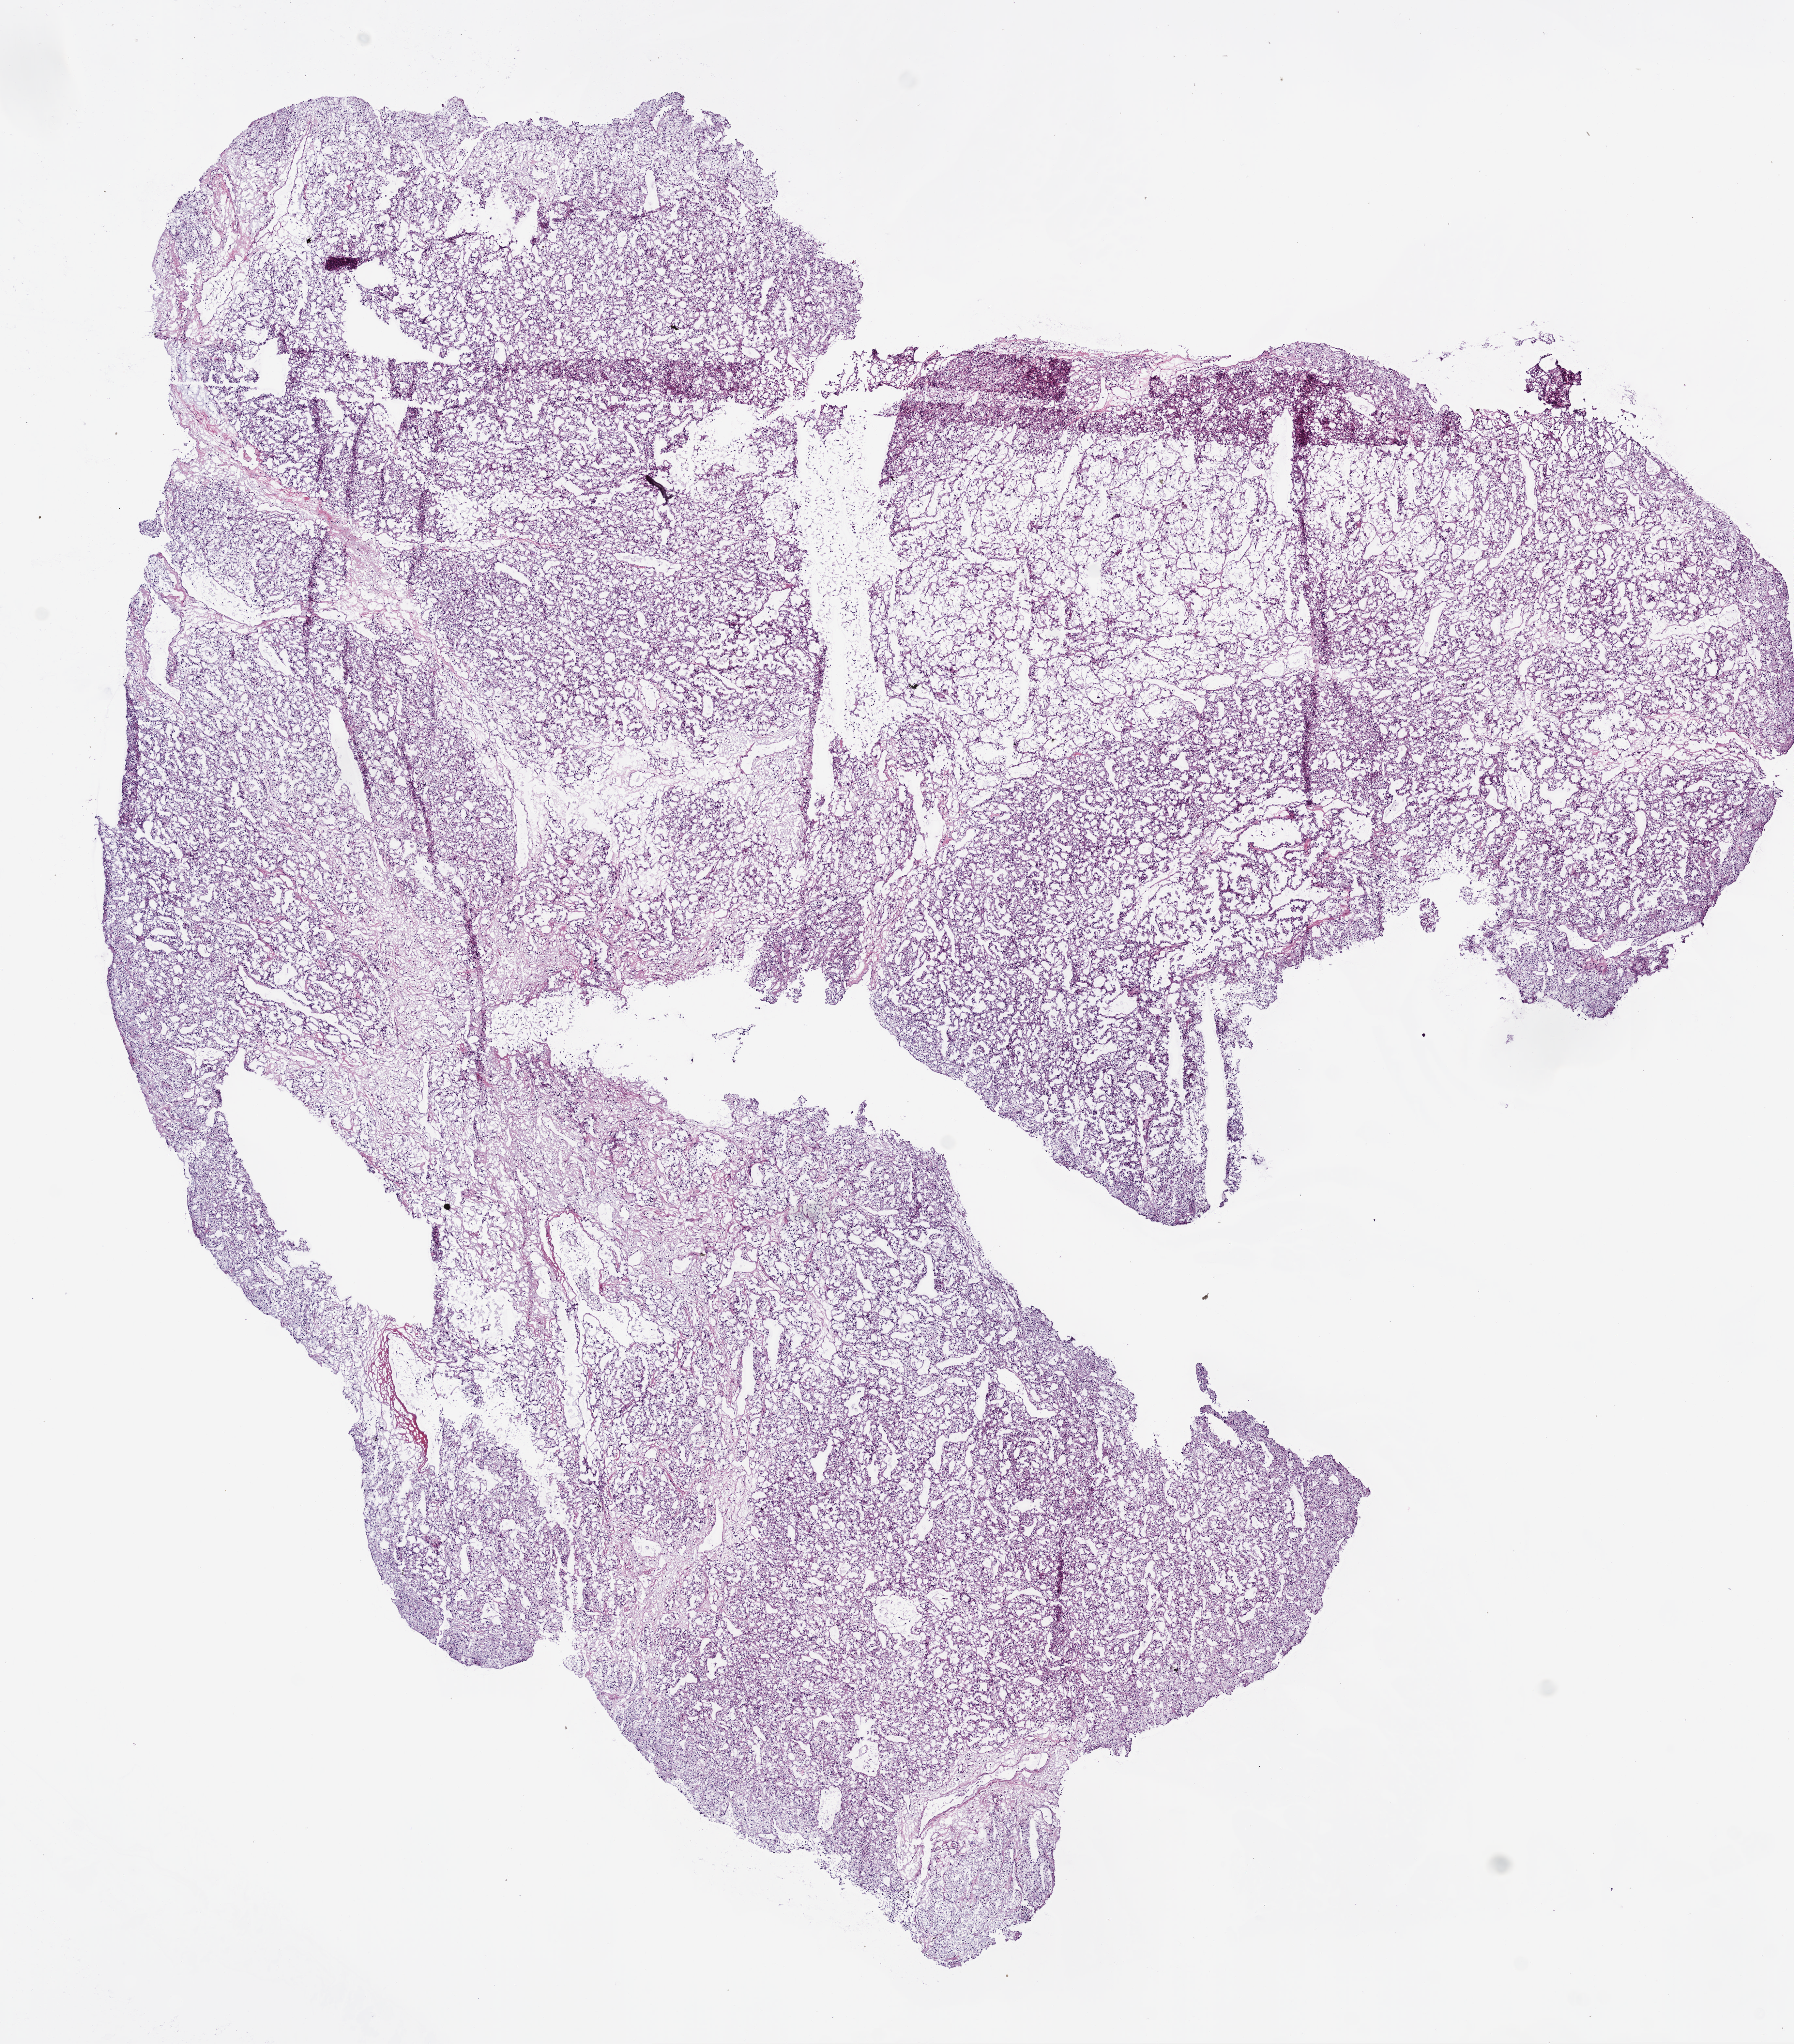
Whole-slide histology image, H&E, shown as a low-resolution overview of the whole scanned area (about 11.0 x 12.6 mm, from a 20x scan), frozen section from the bottom of the tissue portion, kidney, primary tumour sample. Male patient; age at initial diagnosis 57 years. Histologic grade: G3 (poorly differentiated). Composition of this section per pathologist review: tumour cells 90%, tumour nuclei 85%, normal cells 0%, stromal cells 10%, necrosis 0%.
* laterality: left
* AJCC pathologic stage: III
* pathologic diagnosis: Clear cell adenocarcinoma, NOS